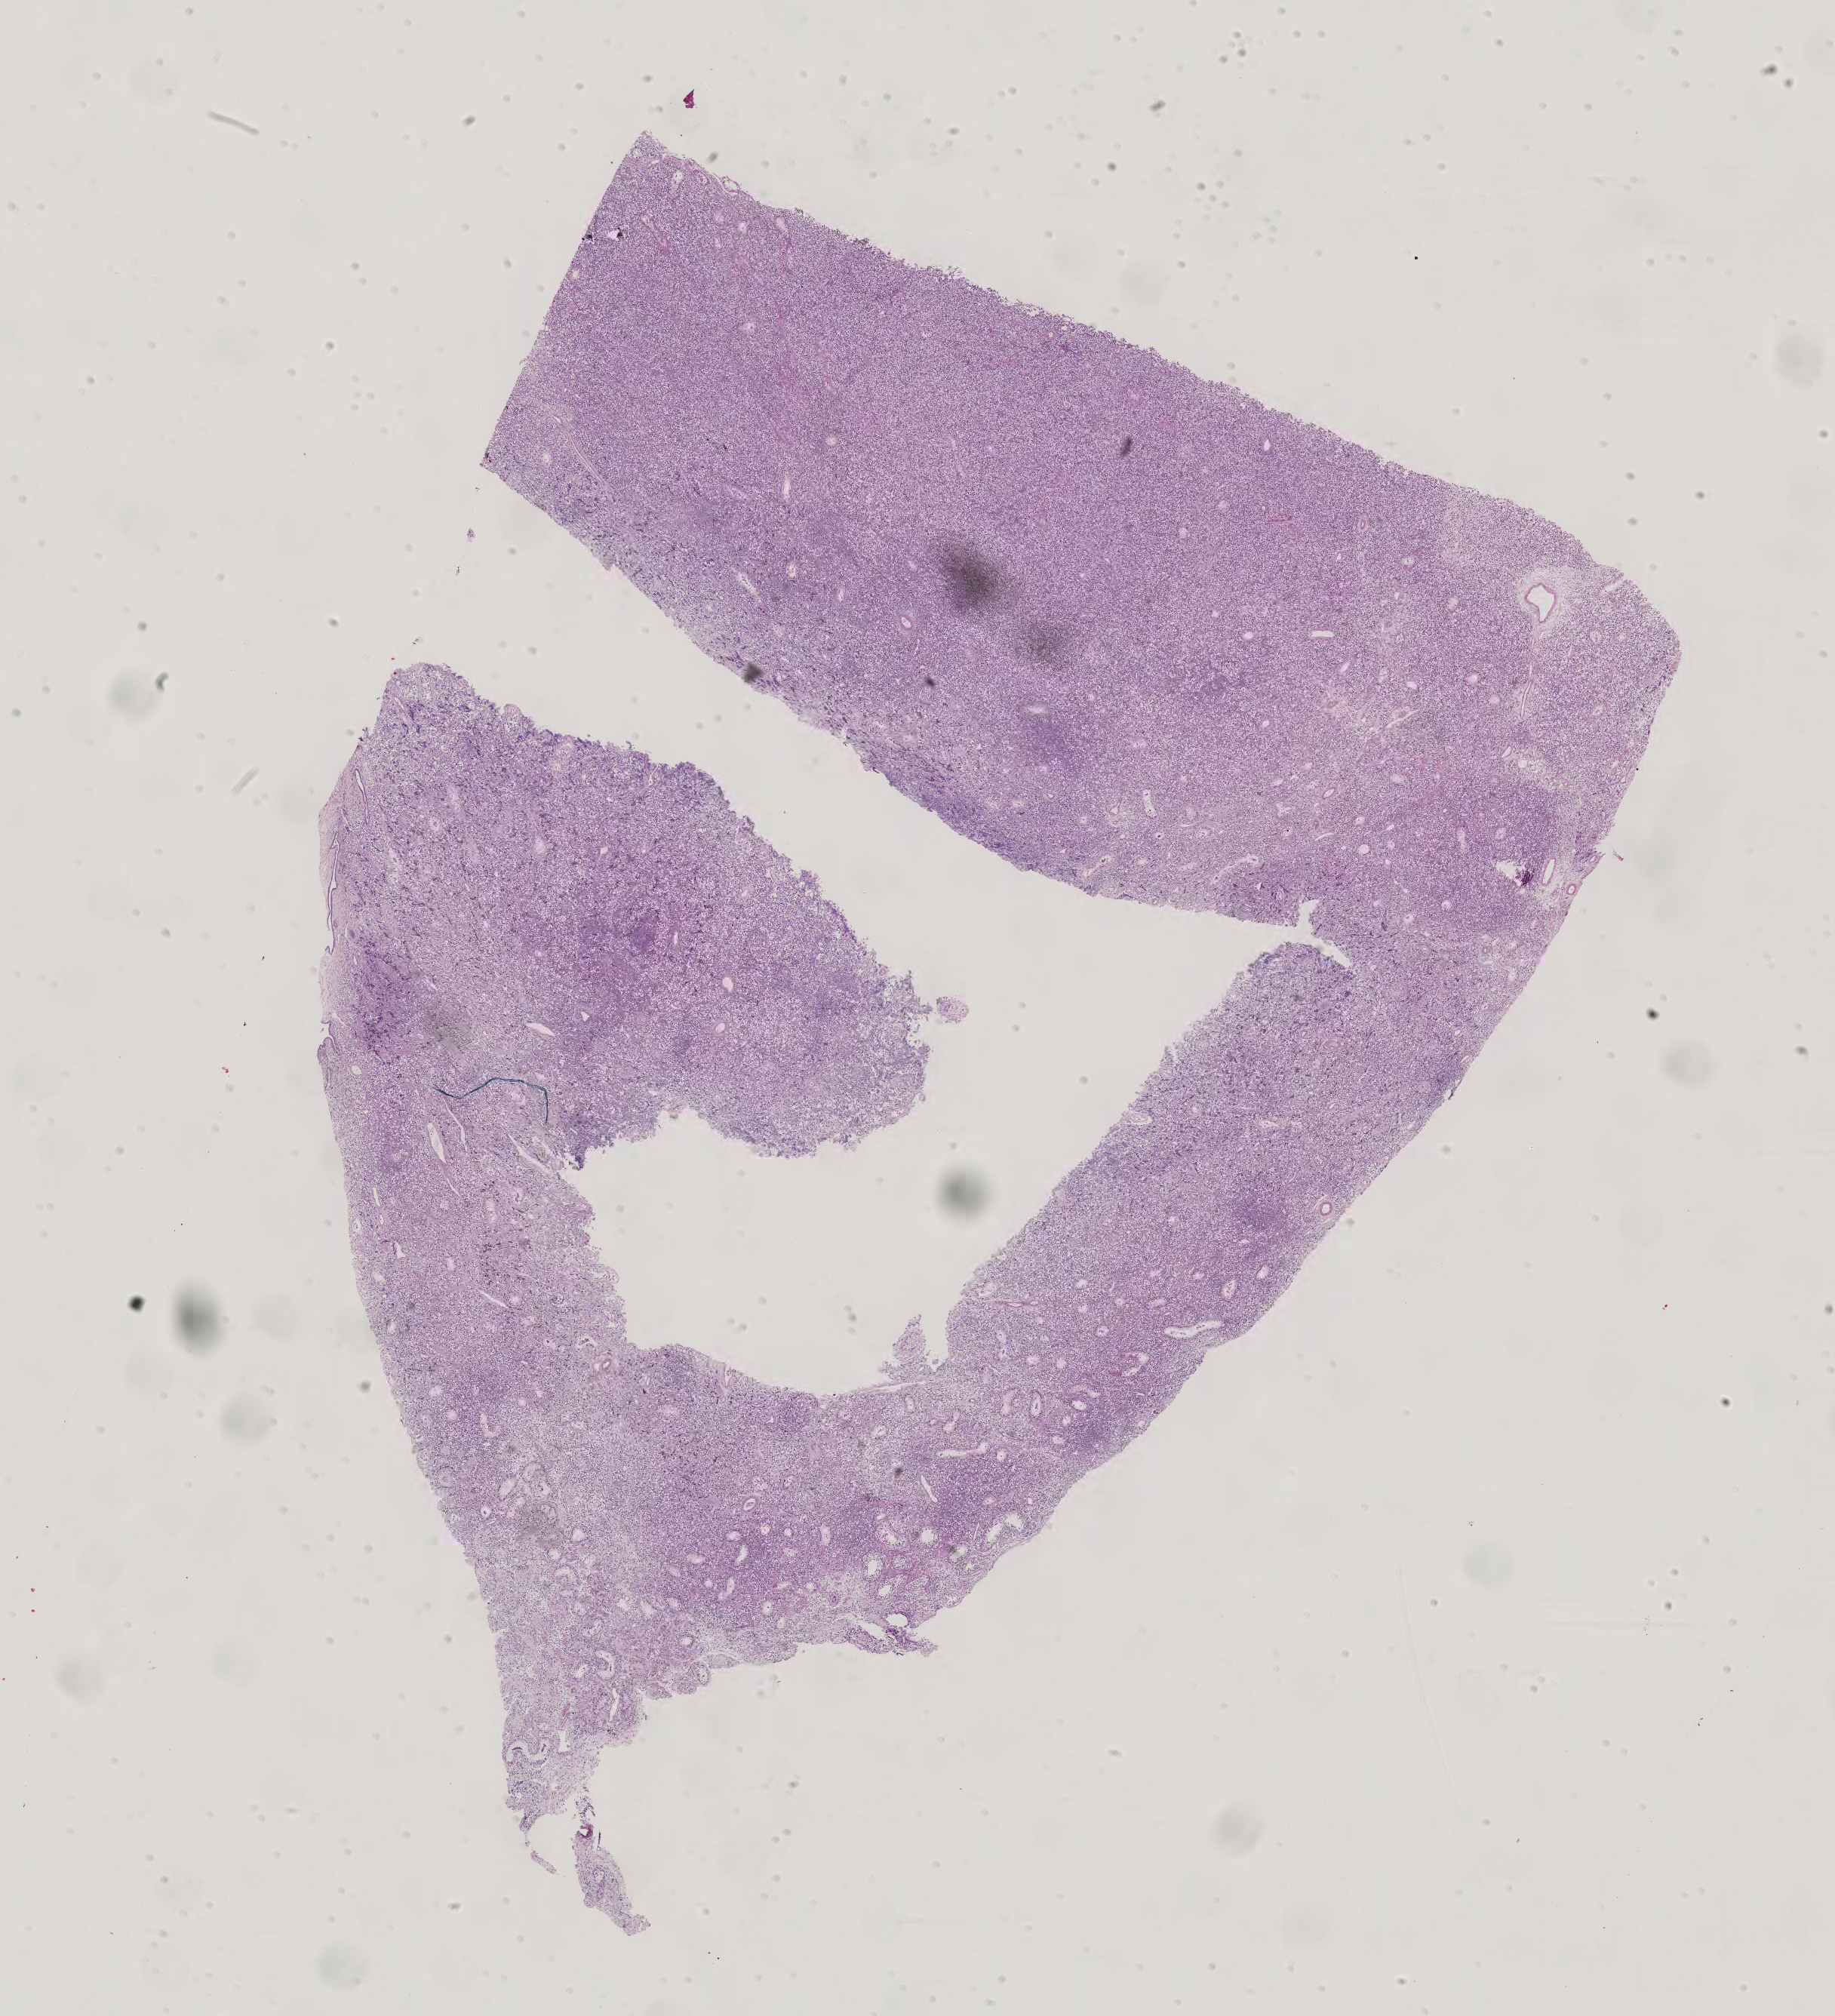
Digitized H&E tissue section (whole slide), a low-resolution overview of the entire scanned area, about 17.7 x 19.5 mm (from a 40x scan). FFPE section. Sample: additional new primary tumour, testis. Male, age 28 years at initial diagnosis.
This section: additional new primary tumour. Patient diagnosis: Teratoma, benign.